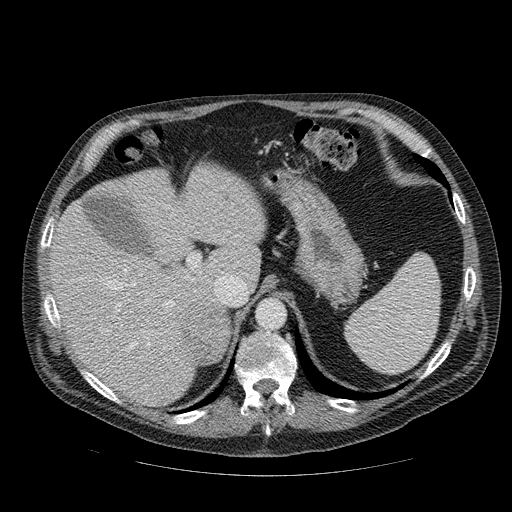
Contrast-enhanced abdominal CT, one axial slice. Slice 69 of 111 in the series (ordered by position). Reconstruction kernel STANDARD. Intravenous contrast given. Soft-tissue window (W 400 / L 40 HU). 2.5 mm slice thickness. 512 × 512 image matrix, field of view 420 × 420 mm. Patient: male, 56 years. Case-level facts recorded for this patient, not image findings: diagnosis: adrenocortical carcinoma; tumour side: right adrenal; tumour size at pathology: 9 cm; Ki-67 index: 48 %; stage (as recorded): 4.
Annotated regions visible in this slice (semi-automatic segmentation, software-assisted and operator-edited):
- mass: bounding box [x1, y1, x2, y2] px = [180, 299, 228, 363]